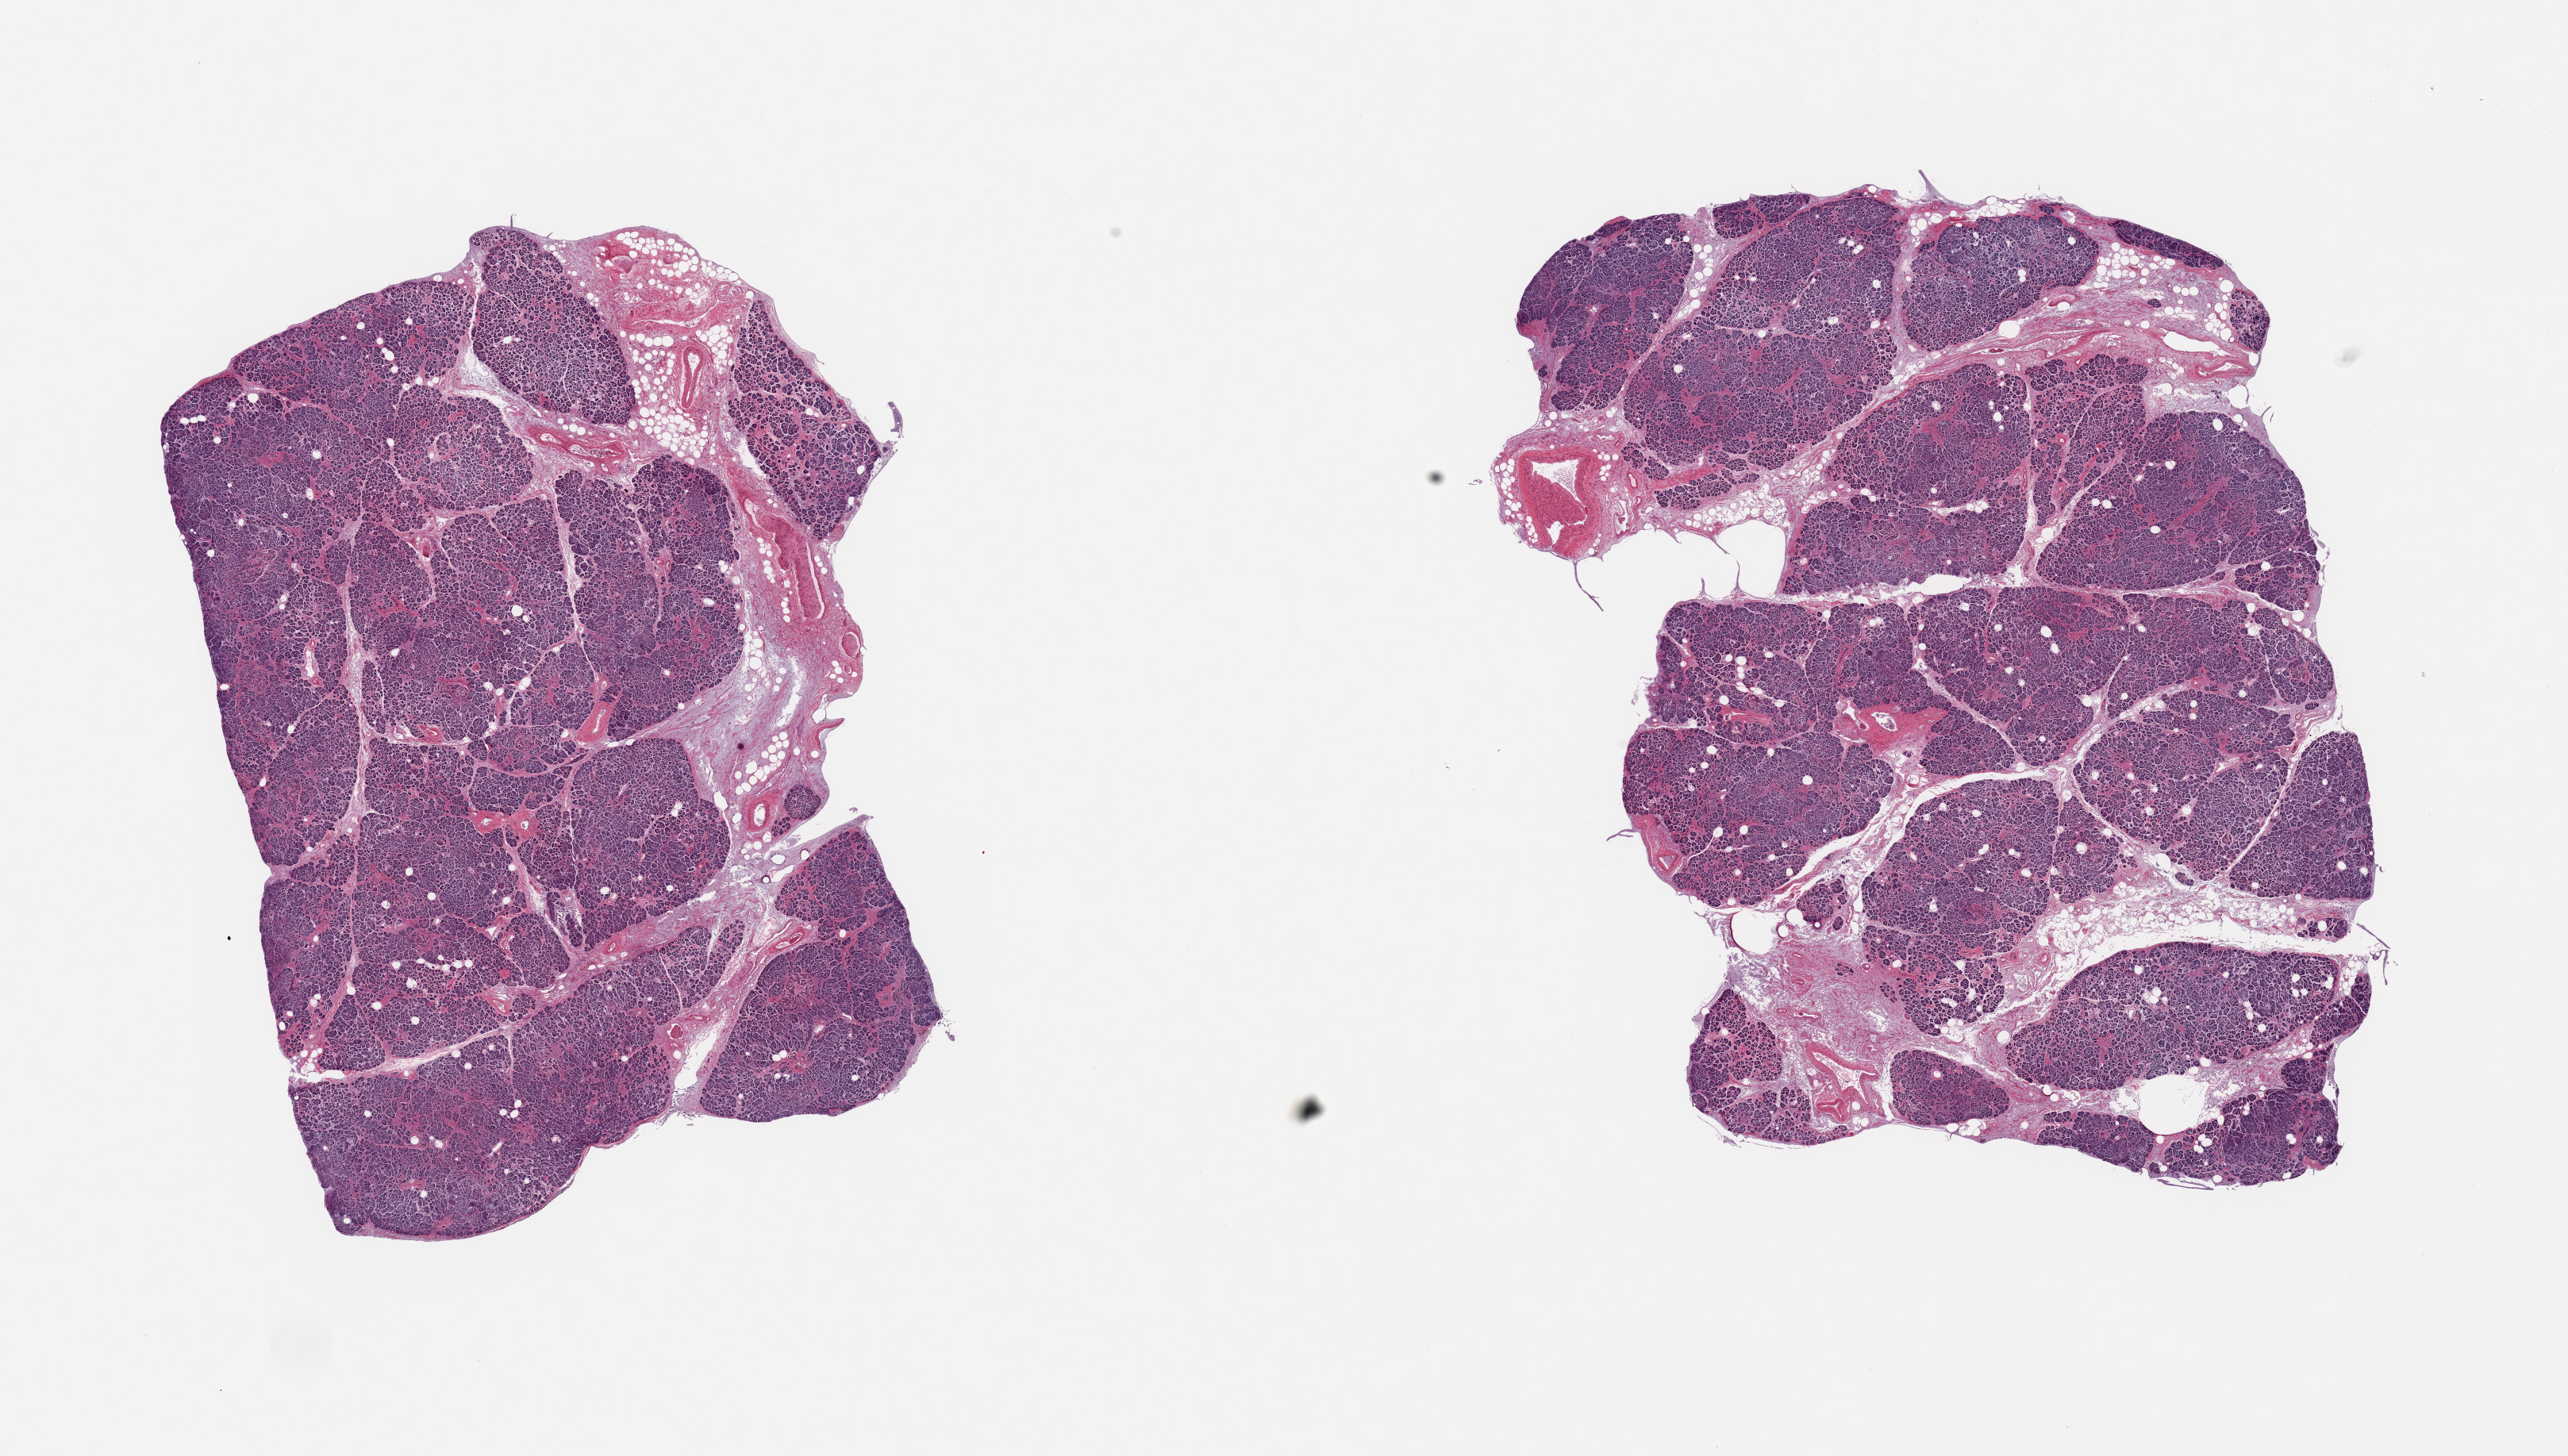
Digitized hematoxylin and eosin (H&E)-stained section — shown as a low-resolution overview of the whole scanned area (about 25.6 x 14.5 mm, from a 20x scan), PAXgene-fixed paraffin-embedded (PFPE) section, sampled site (target tissue): pancreas, tissue donor sample. Donor: male.
- reviewer comment on this tissue sample: 2 pieces, moderately advanced saponification; Few islets visible, moderately degraded